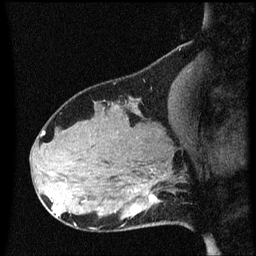
Breast MRI (dynamic contrast-enhanced), one sagittal slice. Slice 22 of 60 in the series (ordered by position). Dynamic contrast-enhanced series, image 2 of 3 at this slice position (ordered by acquisition). 1.5 T. TE 4.2 ms, TR 8.4 ms. 2 mm slice thickness. 256 × 256 image matrix, field of view 200 × 200 mm. Patient: female, 31 years. Case-level facts recorded for this patient, not image findings: setting: breast cancer imaged before/during neoadjuvant chemotherapy; receptor status: HR-positive, HER2-negative.
Outlined on this slice (semi-automatic segmentation, software-assisted and operator-edited):
- analysis volume of interest (the breast-tissue region the enhancement analysis was run in; not a lesion): bounding box <102,166,176,229> (left, top, right, bottom; pixels)
- tumour enhancement mask (voxels above the 70 % enhancement threshold inside the analysis volume of interest): <137,194,156,211>